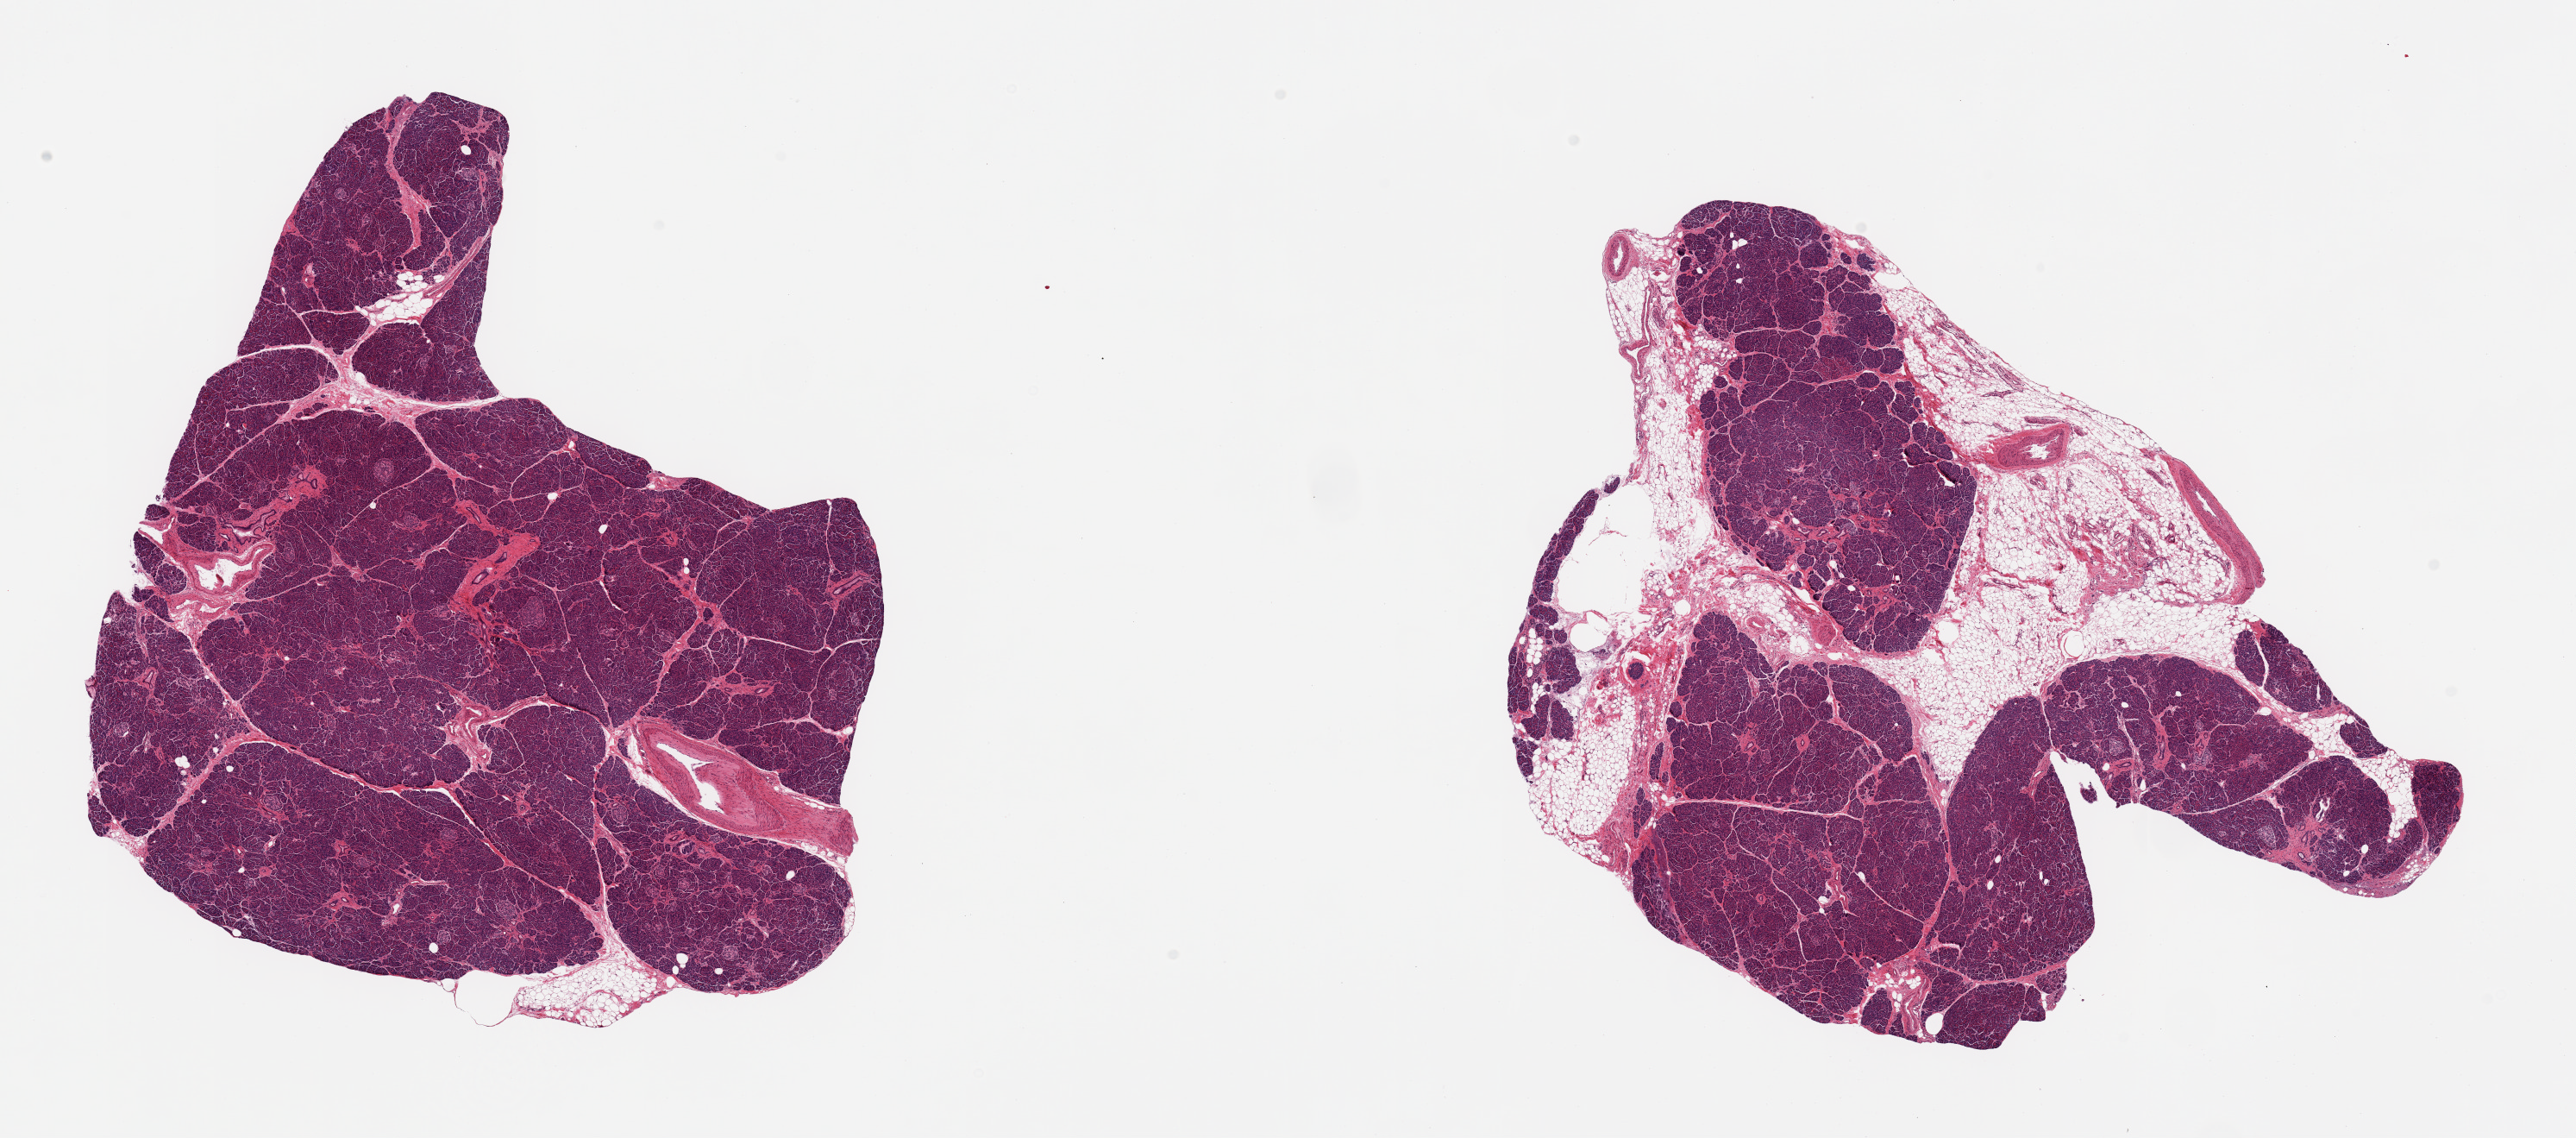
Whole-slide image, haematoxylin and eosin stain, brightfield — low-resolution overview of the scanned area, about 23.6 x 10.4 mm, PAXgene-fixed, paraffin-embedded tissue, target tissue: pancreas, donor tissue sample. Male donor.
• review note (as recorded): 2 pieces; 1 piece has 40% internal fat; other is free of fat